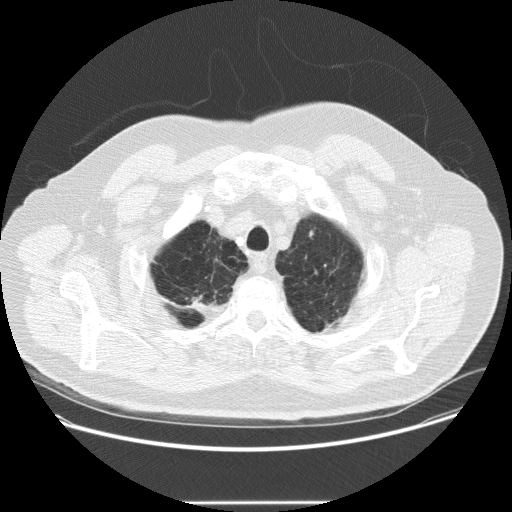
Axial slice from a low-dose chest CT screening exam. Second screening round (one year after baseline). Lung window (W 1500 / L -600 HU). 2.5 mm slice thickness. 512 × 512 image matrix. Male, age 64 years at enrolment. Current smoker at enrolment.
Lesion marked by an expert reader, bounding box (x1, y1, x2, y2) in pixels: (297, 223, 326, 250). The exam's reader record, not a measurement of the box and not confirmed to be the same lesion: non-calcified nodule or mass ≥4 mm, left upper lobe, 5 × 3 mm, smooth margins, soft tissue attenuation, pre-existing on the prior screen: no. Lung cancer was diagnosed 300 days after this screen: adenocarcinoma, NOS, left upper lobe, poorly differentiated (G3), stage IA (AJCC 6th edition), 8 mm at pathology.